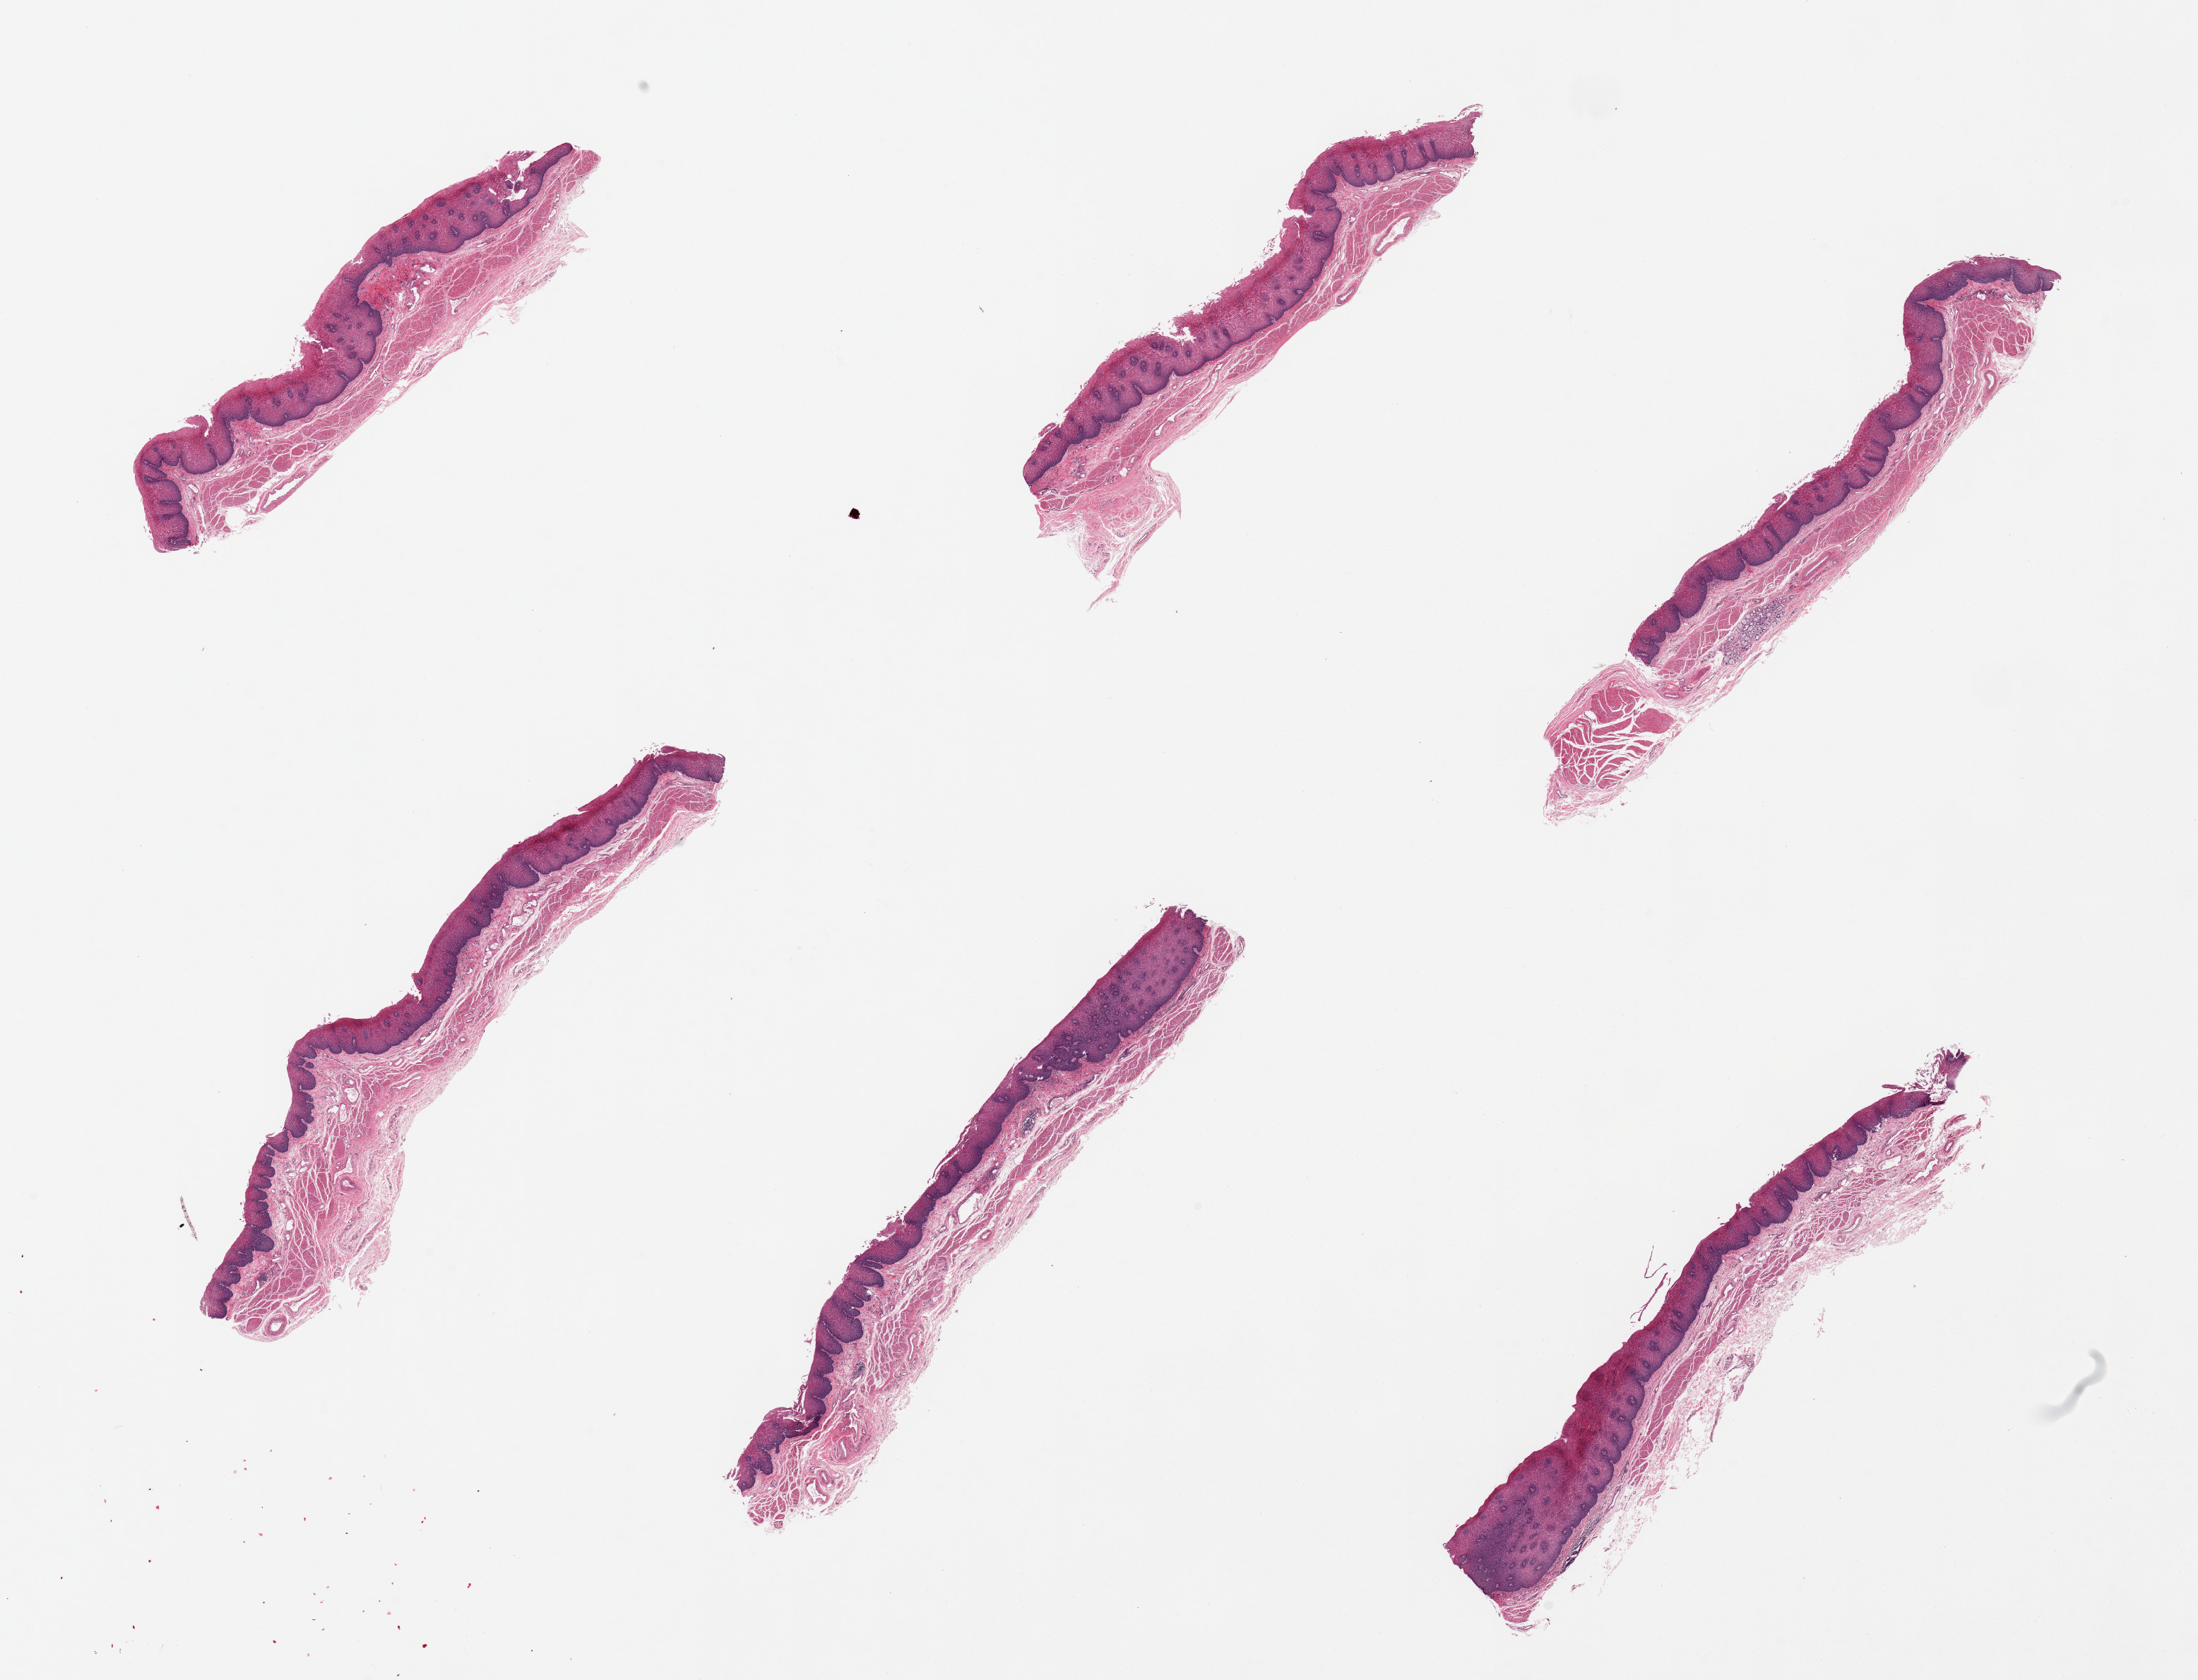
Haematoxylin and eosin whole-slide image, brightfield, a low-resolution overview of the entire scanned area, about 24.6 x 18.8 mm (acquisition: 20x scan), PAXgene-fixed, paraffin-embedded tissue, target tissue: esophageal mucous membrane, tissue donor sample. Male donor.
• pathologist's review note for this sample: 6 pieces; squamous mucosa represents from 15-30% of thickness; small portion of muscularis propria on one piece